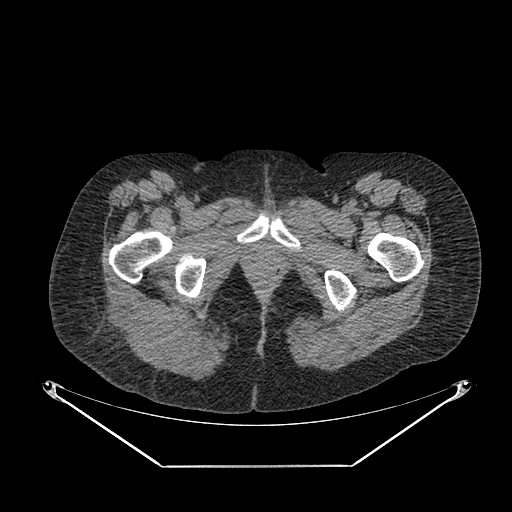
CT of an extremity soft-tissue mass (from a PET/CT study), one axial slice. Slice 44 of 267 in the series (ordered by position). Soft-tissue window (W 400 / L 40 HU). 512 × 512 image matrix, field of view 500 × 500 mm. Female patient. Case-level facts recorded for this patient, not image findings: histological type: spindle cell suggestive of myxofibrosarcoma; grade: intermediate; site of the primary tumour: right buttock.
Outlined on this slice (expert contour drawn on MRI and transferred to this co-registered scan by the dataset authors):
- gross tumour volume (mass): bounding box [x1, y1, x2, y2] px = [114, 301, 126, 318]